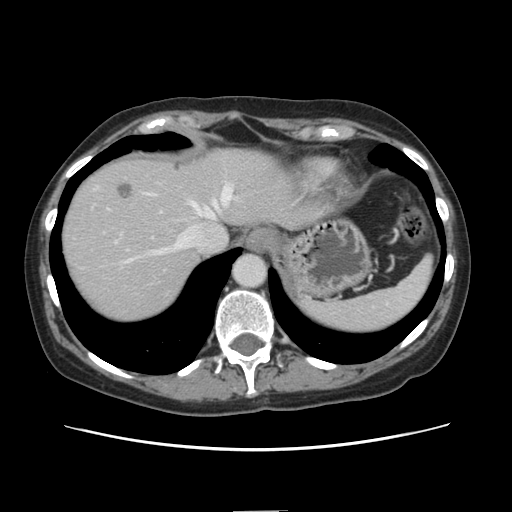
Contrast-enhanced abdominal CT, one axial slice. Soft-tissue window (W 400 / L 40 HU). 2.5 mm slice thickness. 512 × 512 image matrix, field of view 350 × 350 mm. Female patient, age 63 years. Case-level facts recorded for this patient, not image findings: diagnosis: colorectal cancer liver metastases, imaged before liver resection; multiple liver metastases: yes.
Structures marked on this image (expert manual segmentation):
- hepatic veins: box from (x=141, y=186) to (x=231, y=257) px
- liver: (x=62, y=149)–(x=315, y=324)
- planned liver remnant (the part of the liver to remain after resection): (x=201, y=149)–(x=313, y=228)
- portal vein (with intrahepatic branches): (x=126, y=194)–(x=152, y=262)